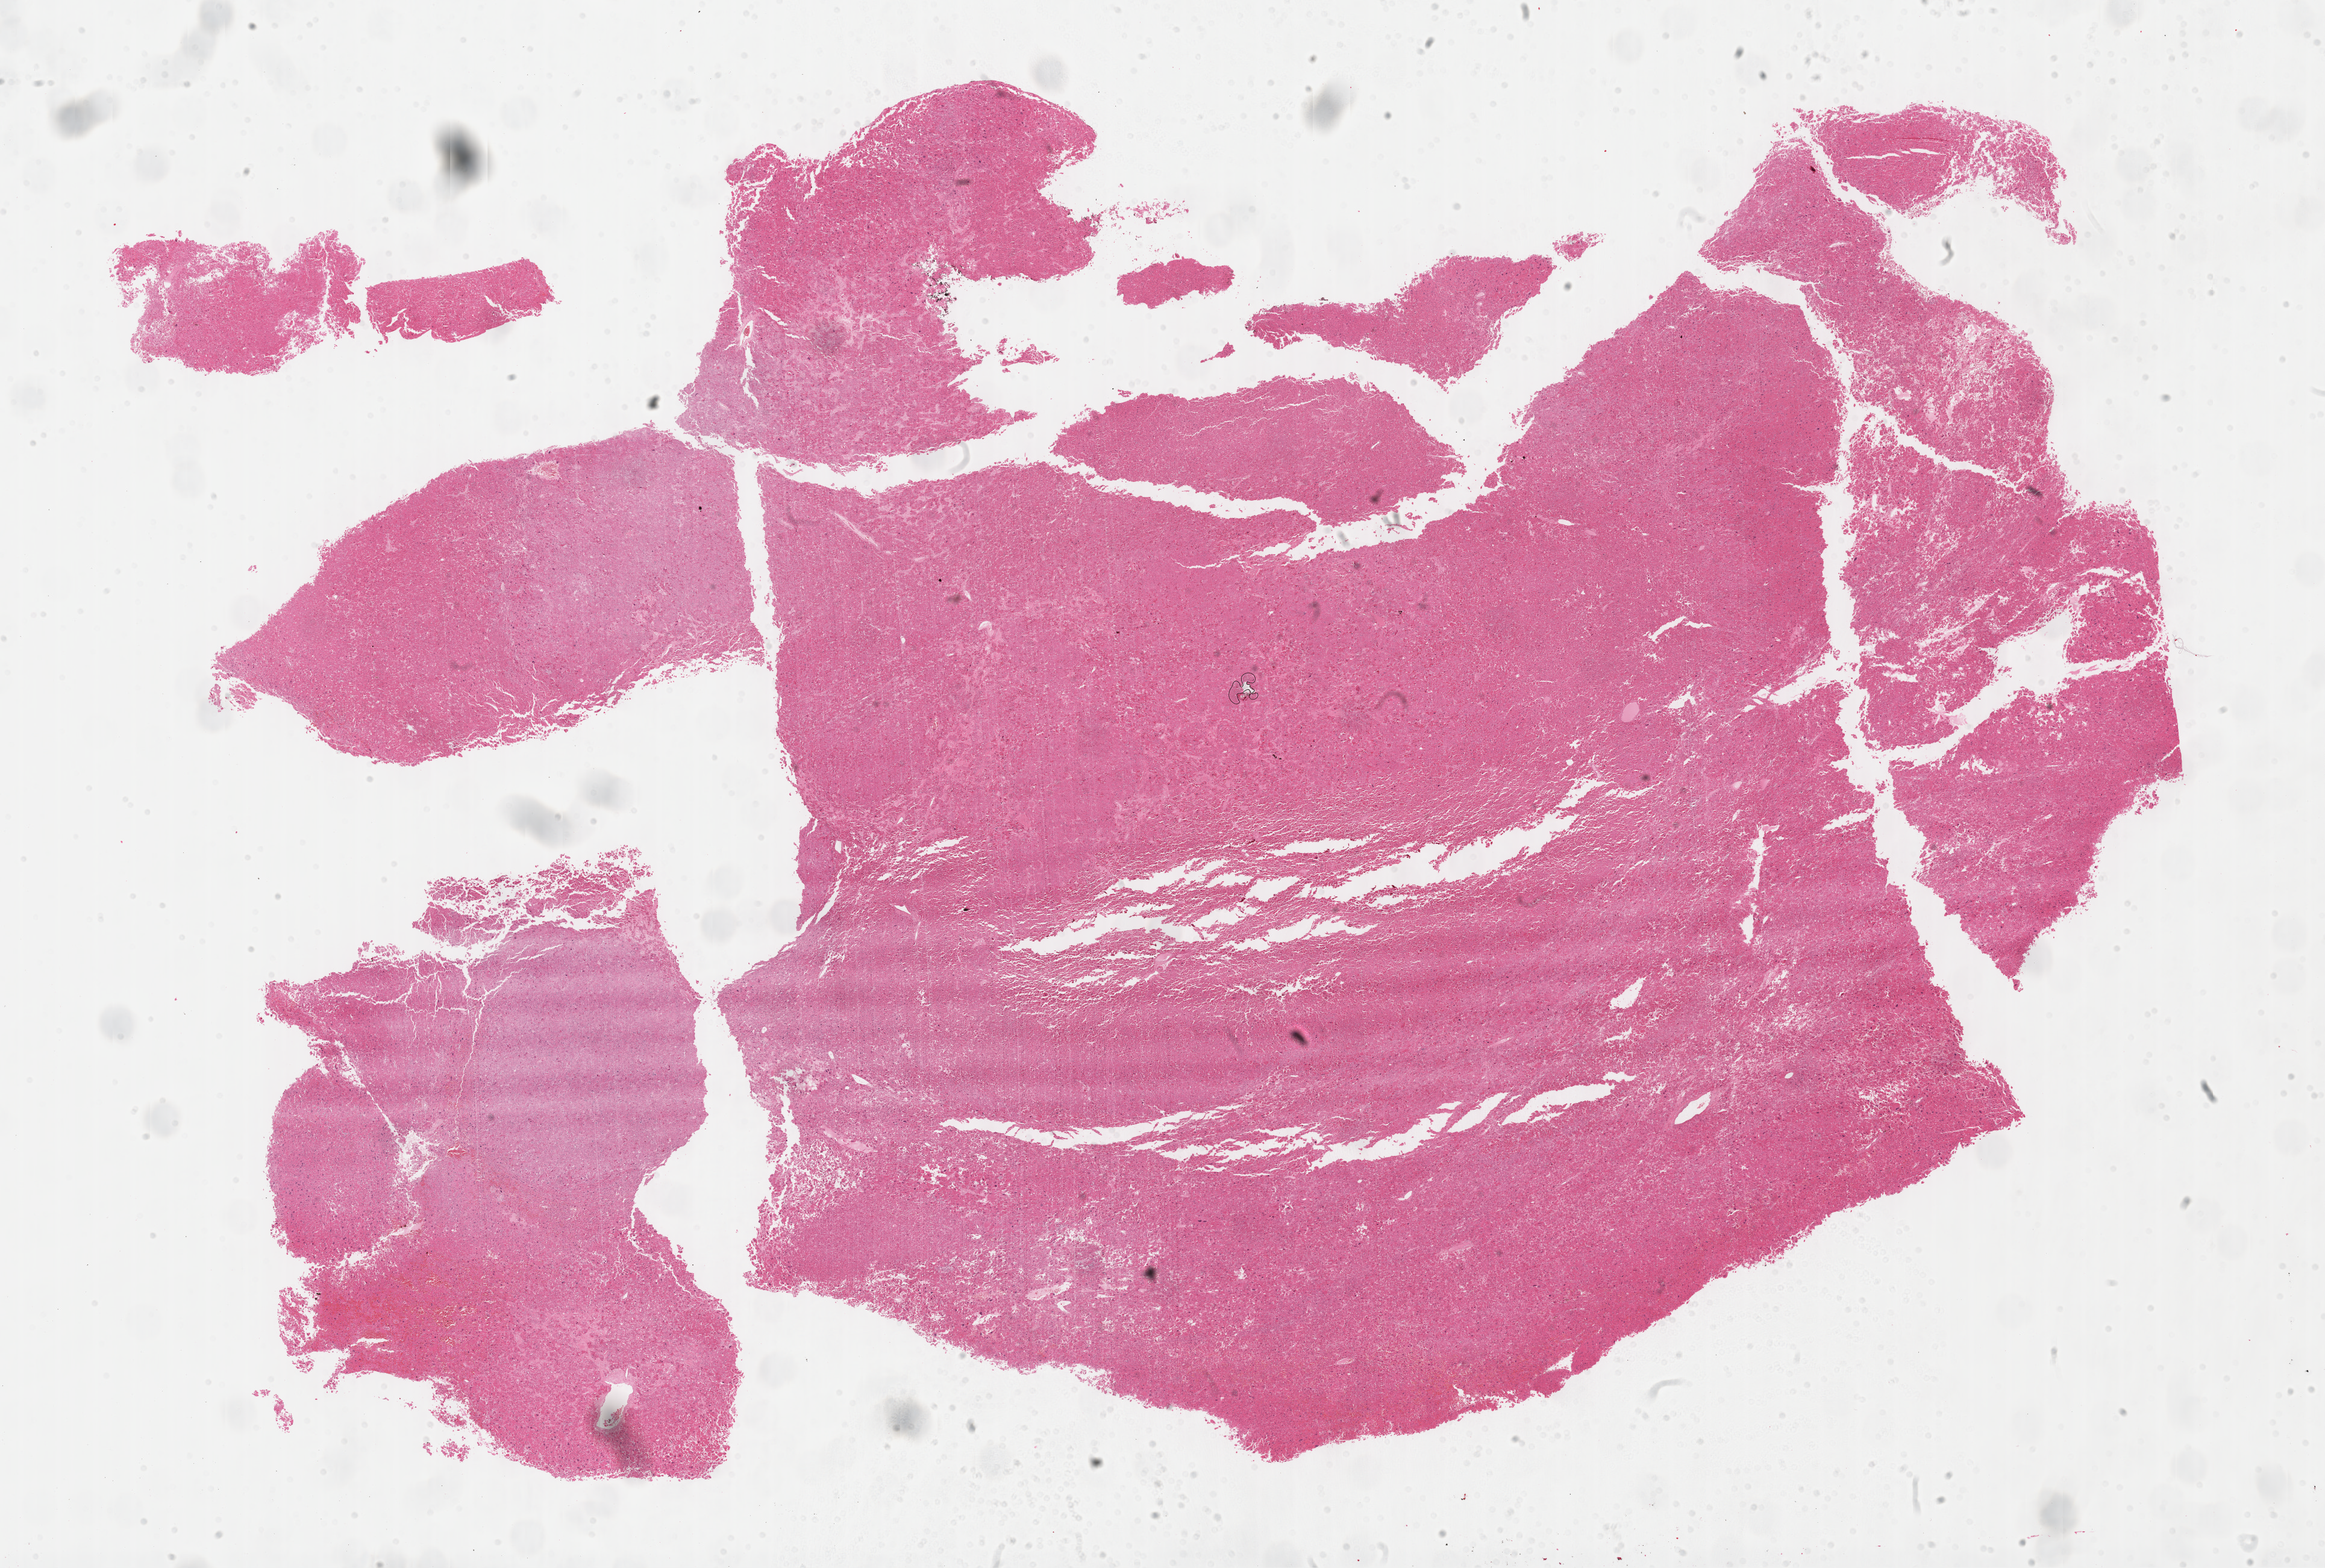
H&E whole-slide image, low-resolution overview of the scanned area, about 31.2 x 21.1 mm. Formalin-fixed paraffin-embedded (FFPE) diagnostic section. Sample: primary tumour, adrenal cortex. Female patient; age at initial diagnosis 57 years.
Diagnosis: Adrenal cortical carcinoma.